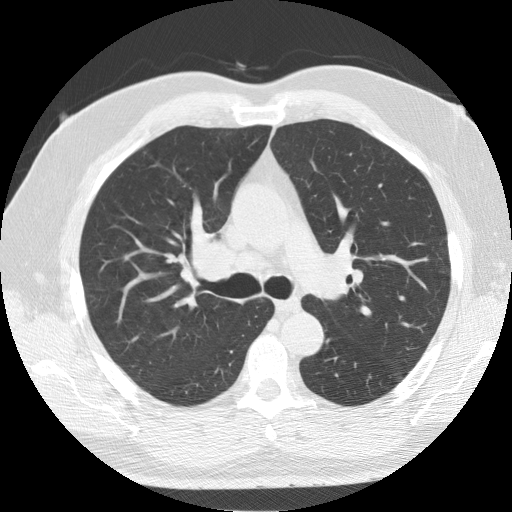
Low-dose screening chest CT, one axial slice; slice 92 of 139 in the series (ordered by position); lung window (W 1500 / L -600 HU); 2.5 mm slice thickness; 512 × 512 image matrix.
Annotated regions visible in this slice (manually delineated by an expert):
- lesion 1 (tumor, upper lobe of right lung): bounding box (x1, y1, x2, y2) in pixels: (189, 238, 236, 282)